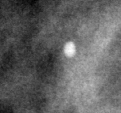
Region of interest cut from a scanned film mammogram (one marked finding), right breast, MLO view.
Finding: calcifications, morphology round and regular / lucent center; BI-RADS assessment category 2; benign without callback (not worked up further).